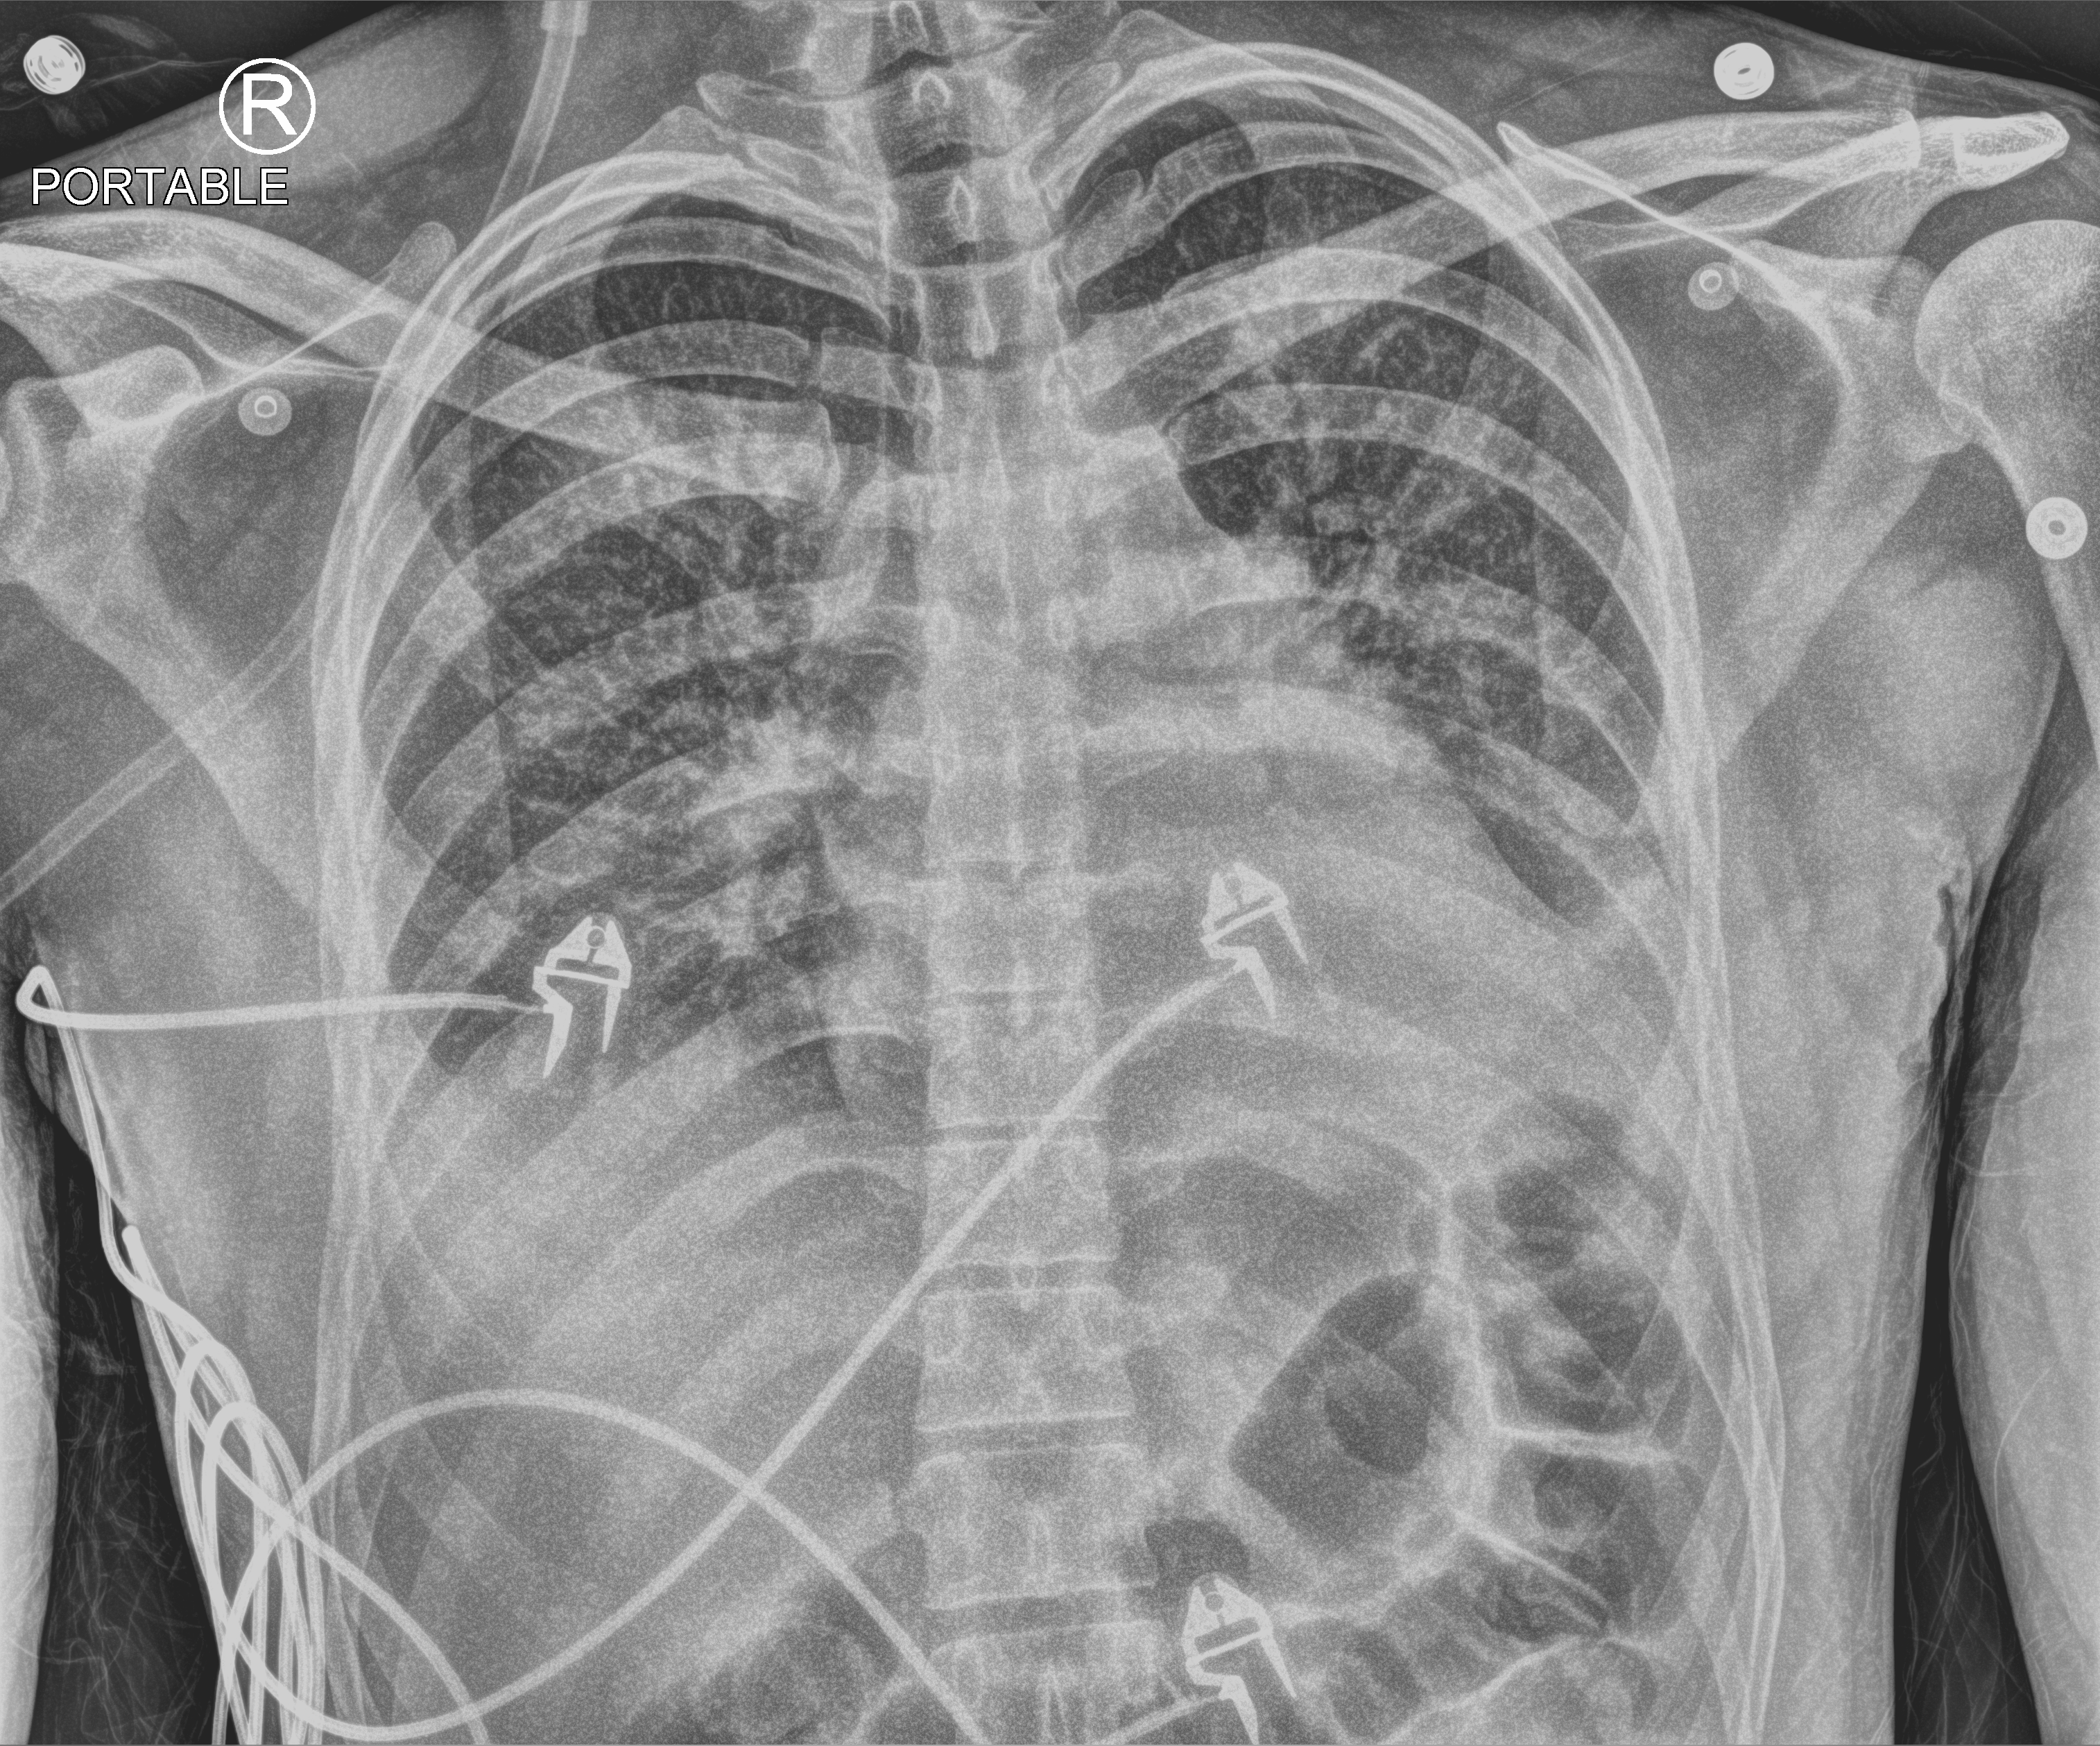
Bedside chest radiograph (computed radiography), anteroposterior (AP) projection. Patient hospitalised with COVID-19; male, aged 18–59 years.
Hospital-stay facts (about this admission, not read from this image; timing relative to this image not recorded): chronic kidney disease (admission record): no; diabetes (admission record): no.